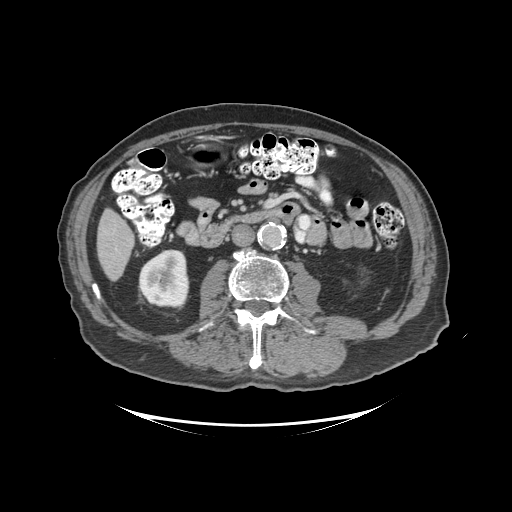
Contrast-enhanced abdominal CT (liver protocol), one axial slice; slice 29 of 99 in the series (ordered by position); reconstruction kernel STANDARD; soft-tissue window (W 400 / L 40 HU); 2.5 mm slice thickness; 512 × 512 image matrix. From the clinical record (not read from this slice): diagnosis: hepatocellular carcinoma (patient treated with transarterial chemoembolisation; whether this scan precedes or follows treatment is not stated here); TNM stage (as recorded): Stage-I; Child-Pugh class: A; tumour differentiation: moderately differentiated; tumour nodularity: uninodular.
Outlined on this slice (semi-automatically segmented with operator editing):
- liver parenchyma outside the tumour (the mass and vessels are separate outlines, so this box may not span the whole liver): box from (x=96, y=208) to (x=134, y=280) px